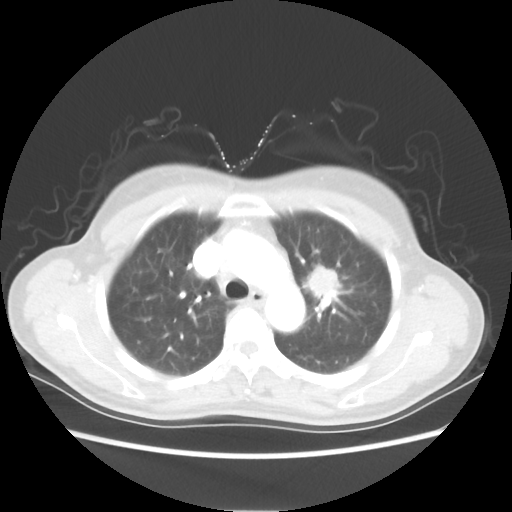
Chest CT, one axial slice; position 39 of 54 along the scan axis; 80 kVp; lung window (W 1500 / L -600 HU); 5 mm slice thickness; 512 × 512 image matrix, field of view 360 × 360 mm. Female patient, age 53 years. Case-level facts recorded for this patient, not image findings: clinical TNM (as recorded): T1c N0 M0.
Annotated regions visible in this slice (bounding box drawn by a radiologist):
- lung tumour (recorded histology: adenocarcinoma): bounding box <298,253,342,311> (left, top, right, bottom; pixels)
- lung tumour (recorded histology: adenocarcinoma): <304,256,343,303>